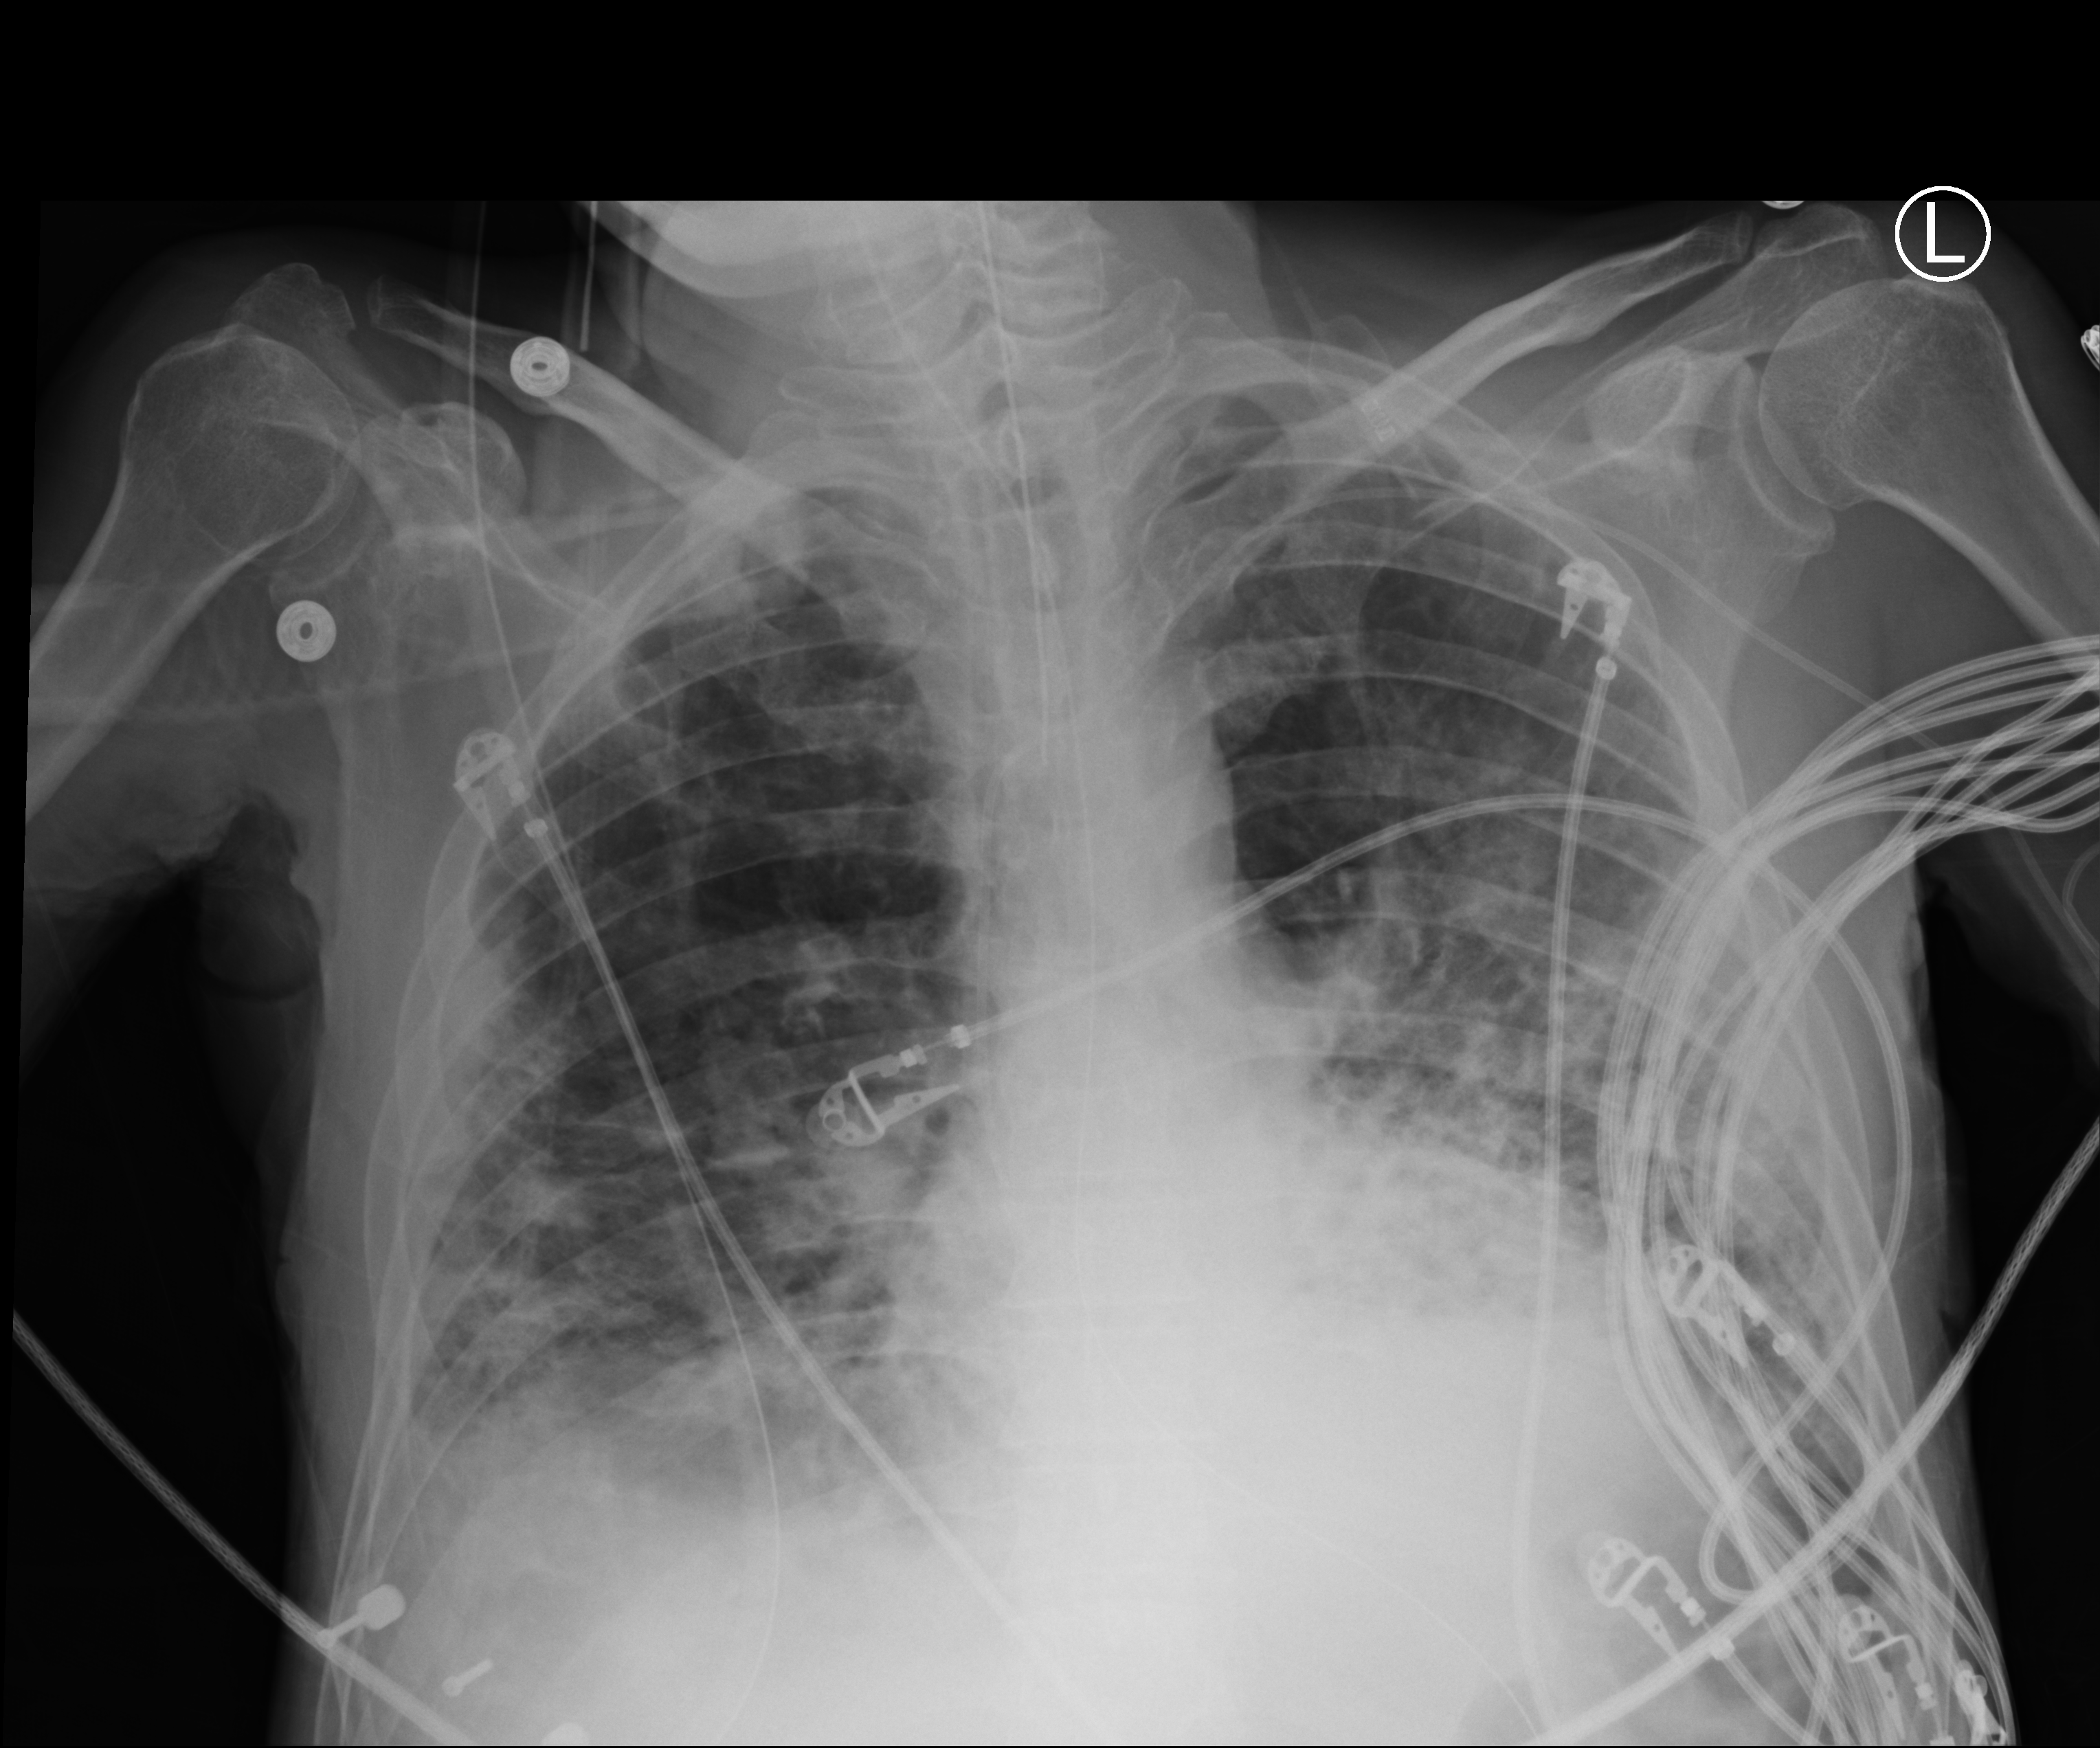
Portable chest radiograph, anteroposterior (AP) projection. Male patient hospitalised with COVID-19, age 18–59 years.
From the hospital-stay record, not from the radiograph (when in the stay this image was taken is not recorded):
- COPD (admission record): no
- admitted to intensive care during this hospital stay: yes
- mechanically ventilated during this hospital stay: yes